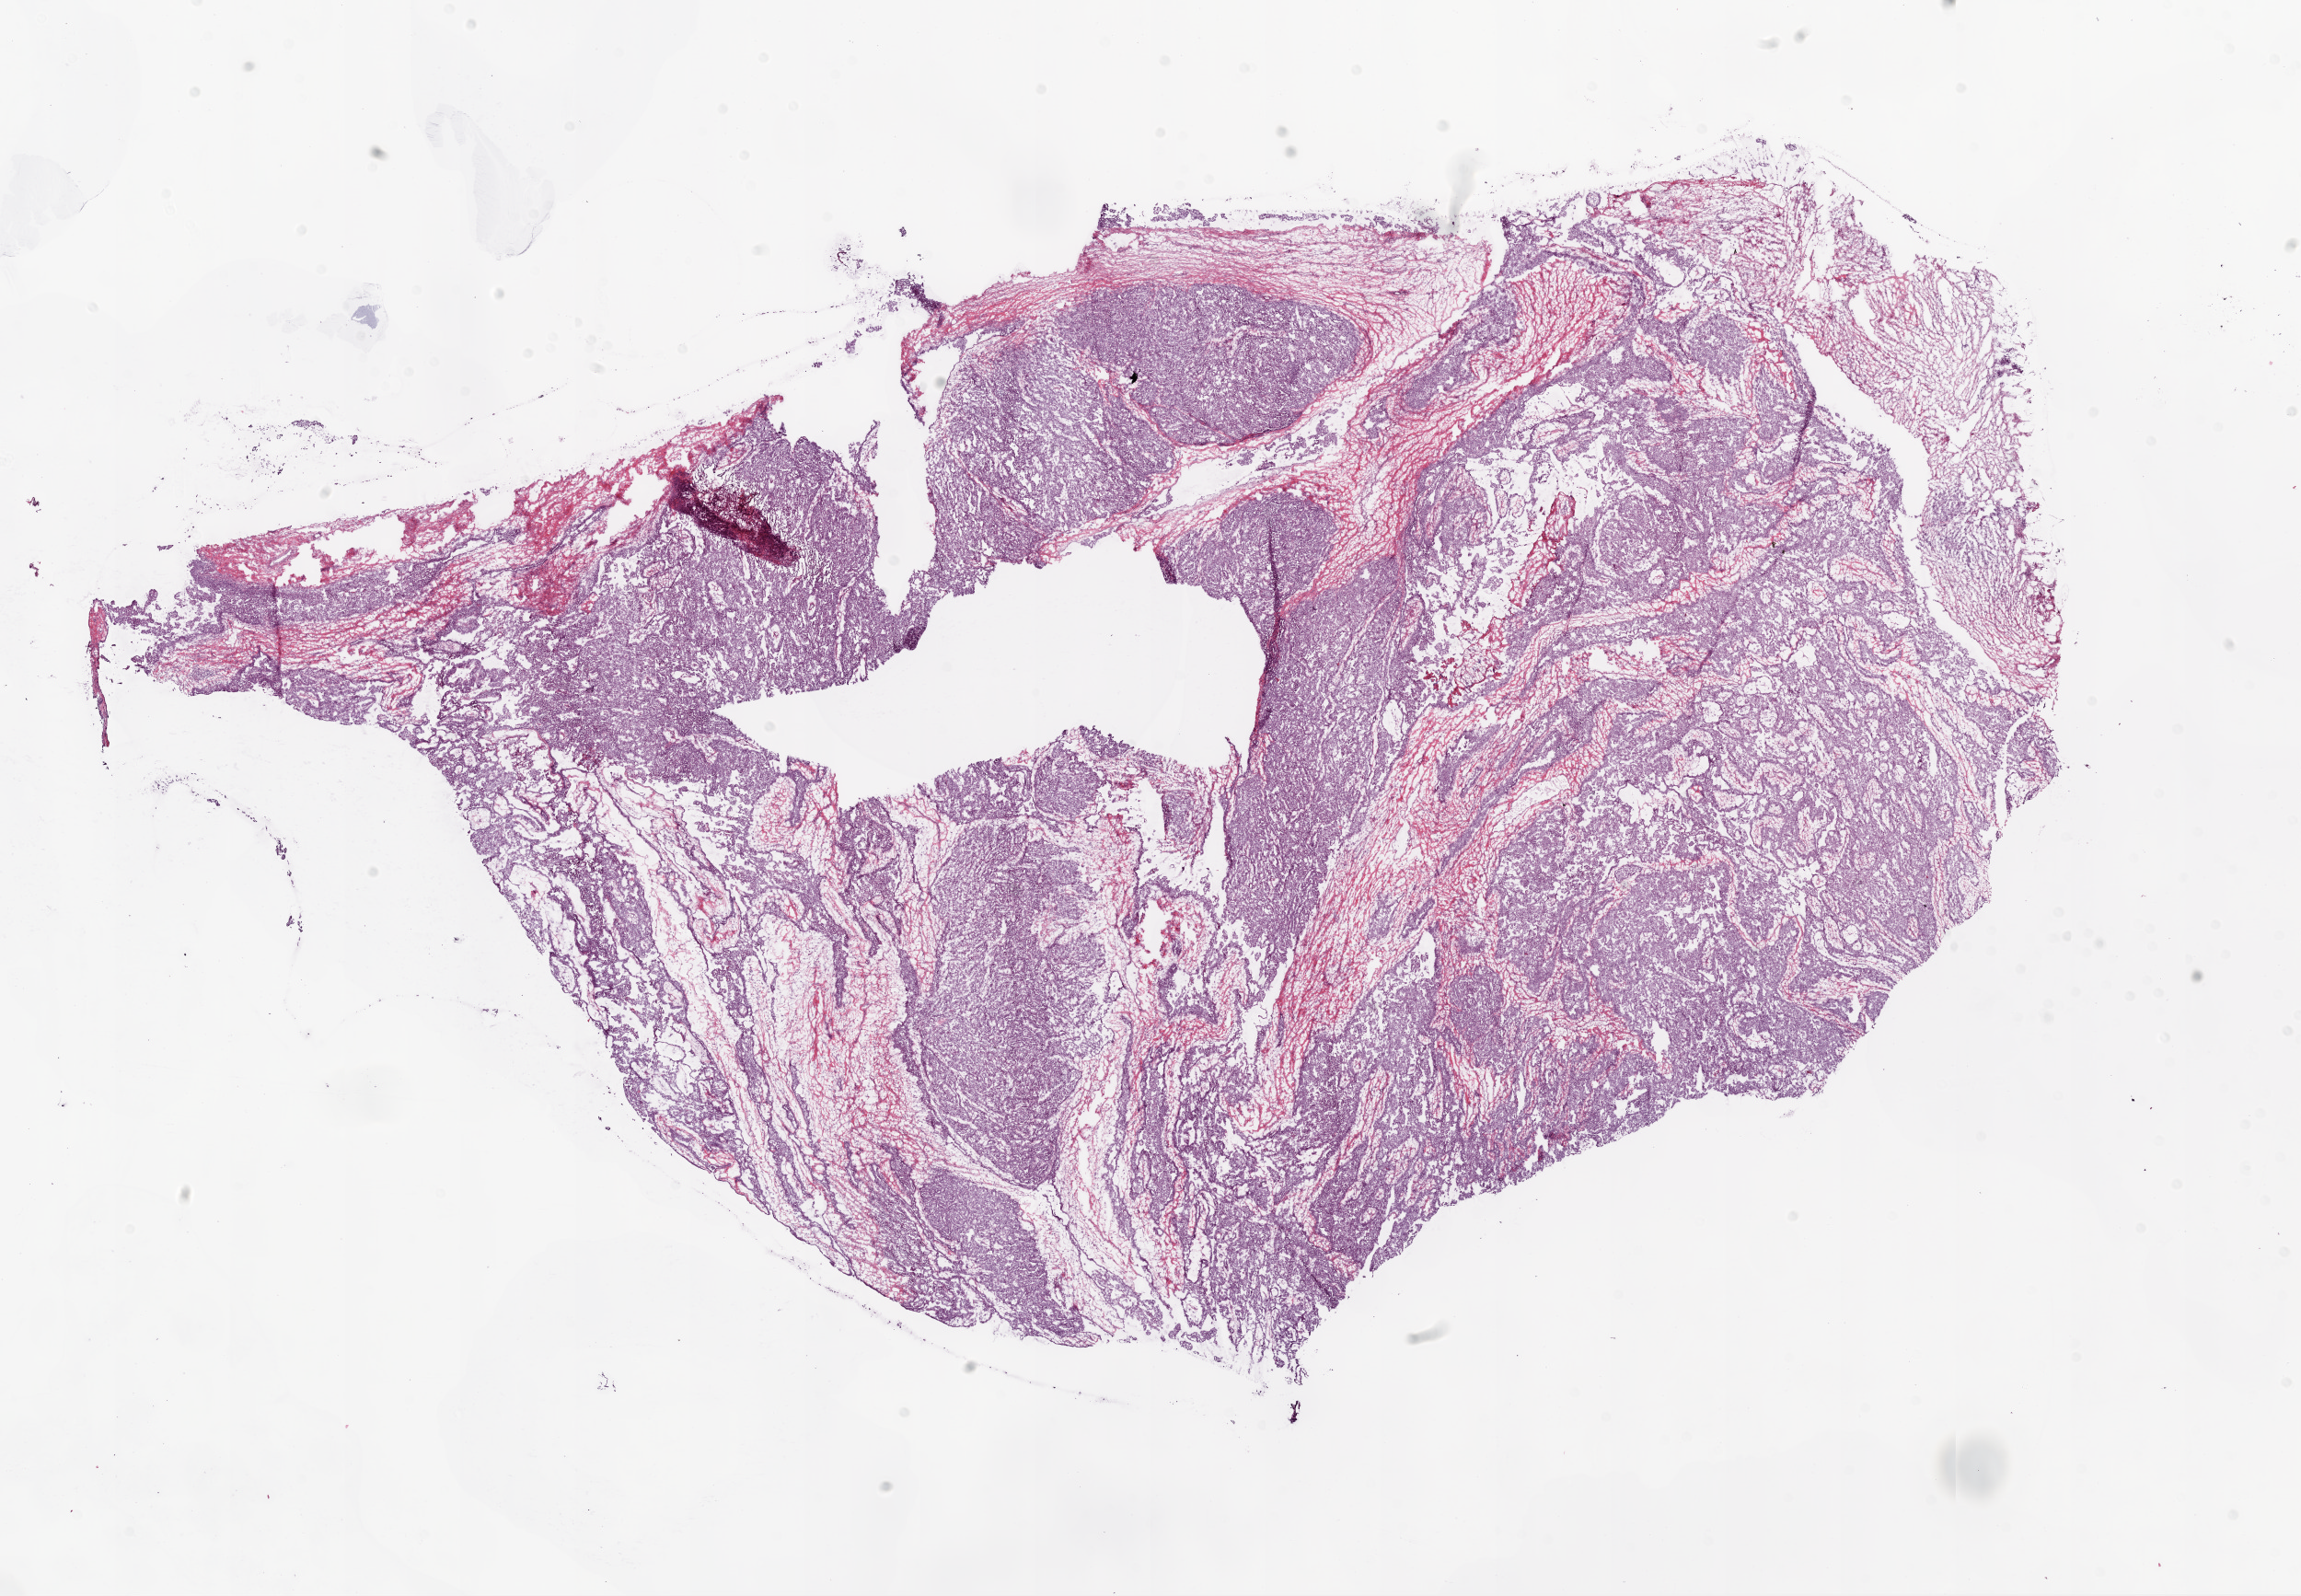
H&E whole-slide image, low-resolution overview of the scanned area, about 20.1 x 13.9 mm (slide scanned at 20x); frozen section from the bottom of the tissue portion; ovary, primary tumour sample. Patient: female, age at initial diagnosis 53 years. Histologic grade: G2 (moderately differentiated). Slide review estimates, as recorded: tumour cells 75%, tumour nuclei 77%, normal cells 15%, stromal cells 5%, necrosis 5%.
- FIGO stage: IIC
- histologic diagnosis: Serous cystadenocarcinoma, NOS
- laterality: bilateral